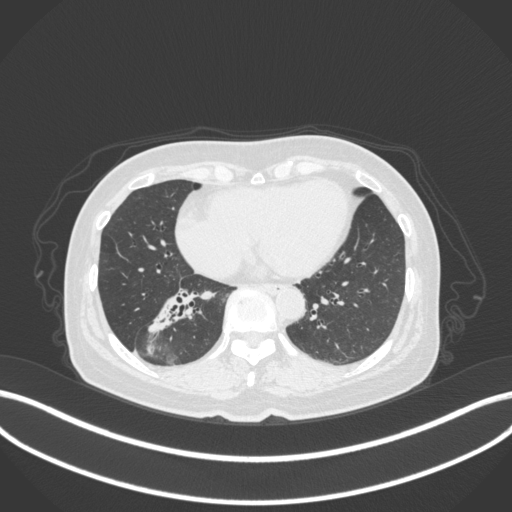
Chest CT, one axial slice; position 144 of 429 along the scan axis; 120 kVp; lung window (W 1500 / L -600 HU); 512 × 512 image matrix, field of view 400 × 400 mm. Female patient, age 67 years. Case-level facts recorded for this patient, not image findings: clinical TNM (as recorded): T1c N1 M0; histopathological grade: G2-3.
Annotated regions visible in this slice (rectangle marked by the reading radiologist):
- lung tumour (recorded histology: adenocarcinoma): box from (x=144, y=282) to (x=199, y=337) px